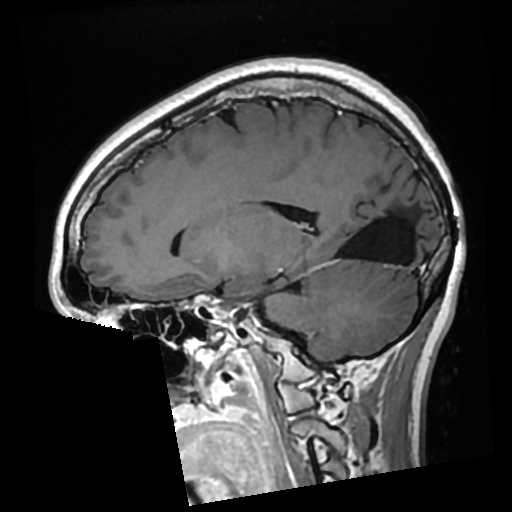
Brain MRI from a brain-tumour surgery series, one sagittal slice; position 116 of 276 along the scan axis; T1-weighted post-contrast; 0.7 mm slice thickness; 512 × 512 image matrix, field of view 250 × 250 mm. From the clinical record (not read from this slice): histopathology: Glioma with ependymal features; WHO grade: 2.
Structures marked on this image (manually delineated by an expert):
- previous resection cavity: bounding box (x1, y1, x2, y2) in pixels: (340, 196, 420, 262)